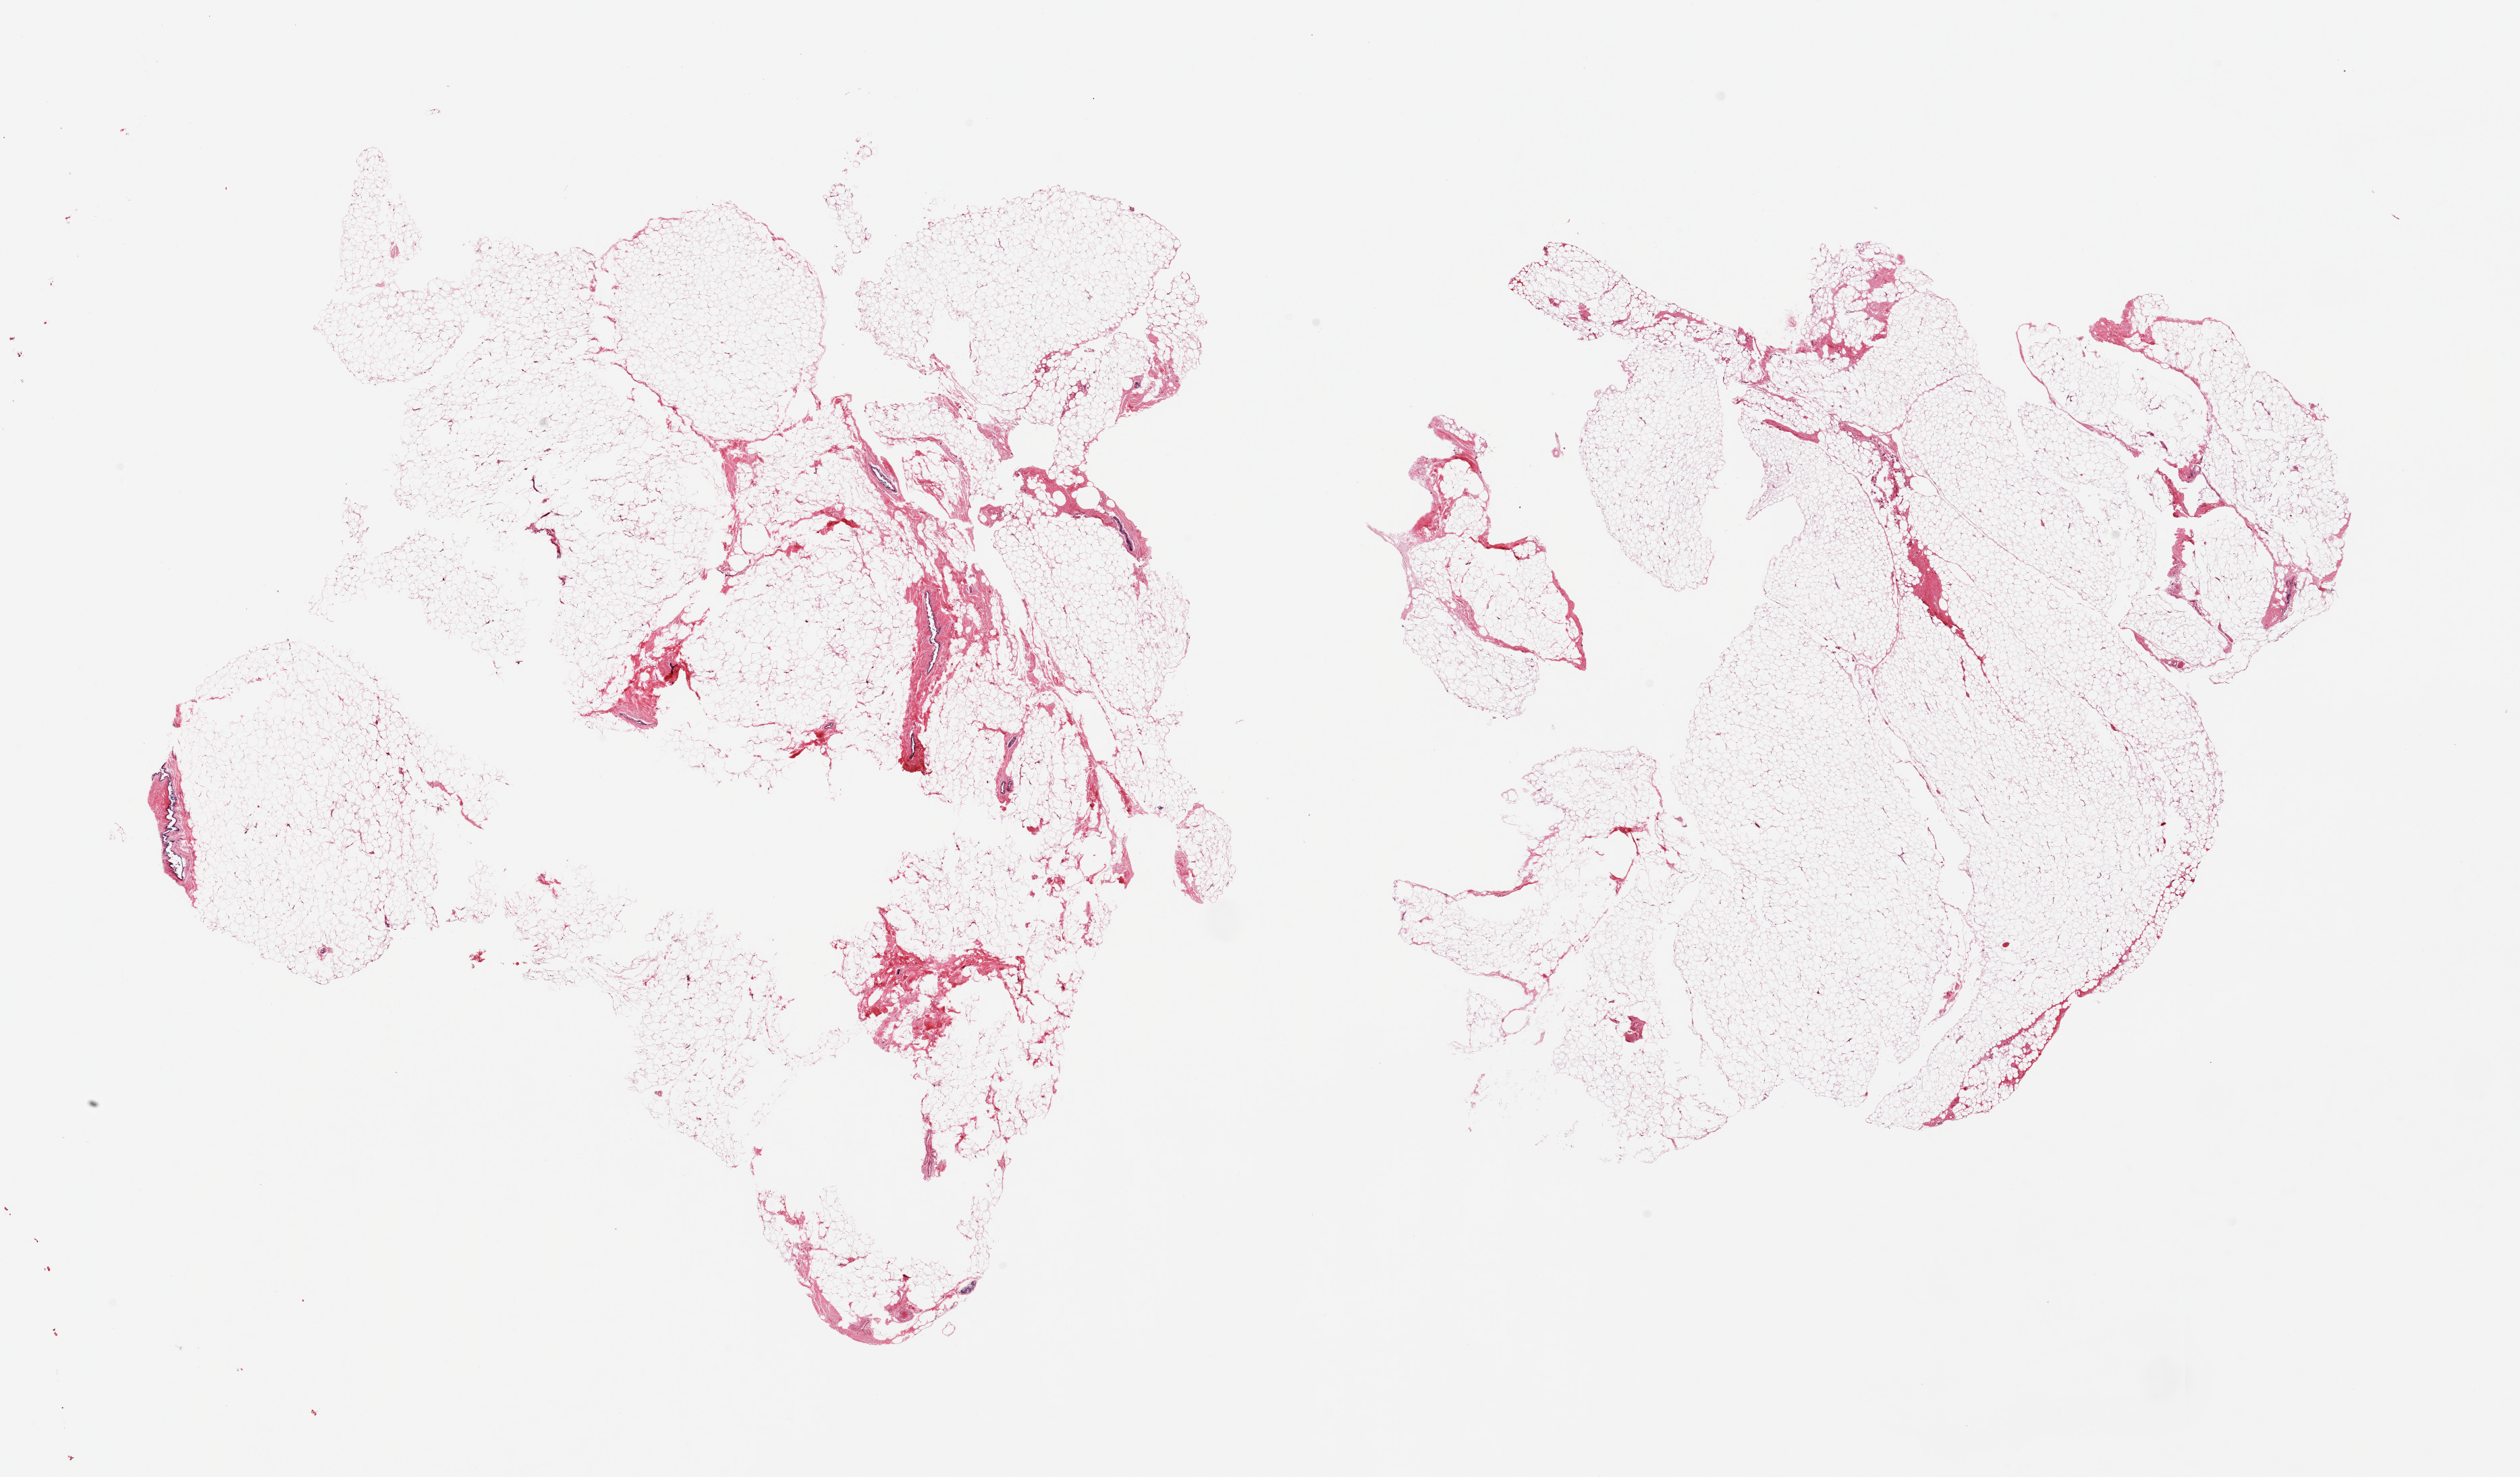
Whole-slide image, haematoxylin and eosin stain, a low-resolution overview of the entire scanned area, about 29.5 x 17.3 mm (from a 20x scan), PAXgene-fixed paraffin-embedded (PFPE) section, sampled site (target tissue): breast, donor tissue sample. Donor sex: female.
* pathologist's review note for this sample: 2 pieces, mainly fibroadipose tissue, rare trace atrophic ductal elements